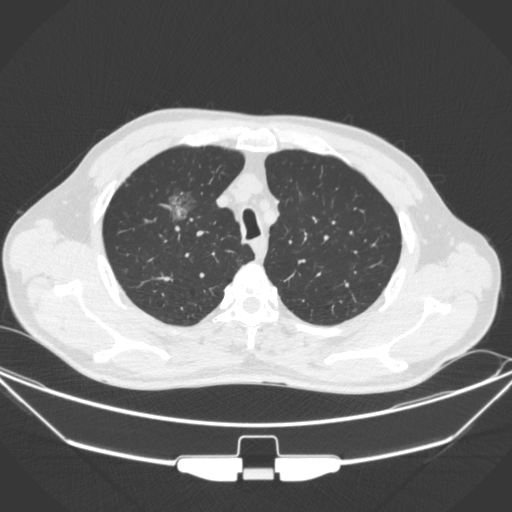
Chest CT, one axial slice. Slice 275 of 355 in the series (ordered by position). Lung window (W 1500 / L -600 HU). 512 × 512 image matrix, field of view 399 × 399 mm. Male patient, age 67 years. Case-level facts recorded for this patient, not image findings: clinical TNM (as recorded): T1c N0 M0.
Outlined on this slice (rectangle marked by the reading radiologist):
- lung tumour (recorded histology: adenocarcinoma): box from (x=157, y=188) to (x=198, y=224) px